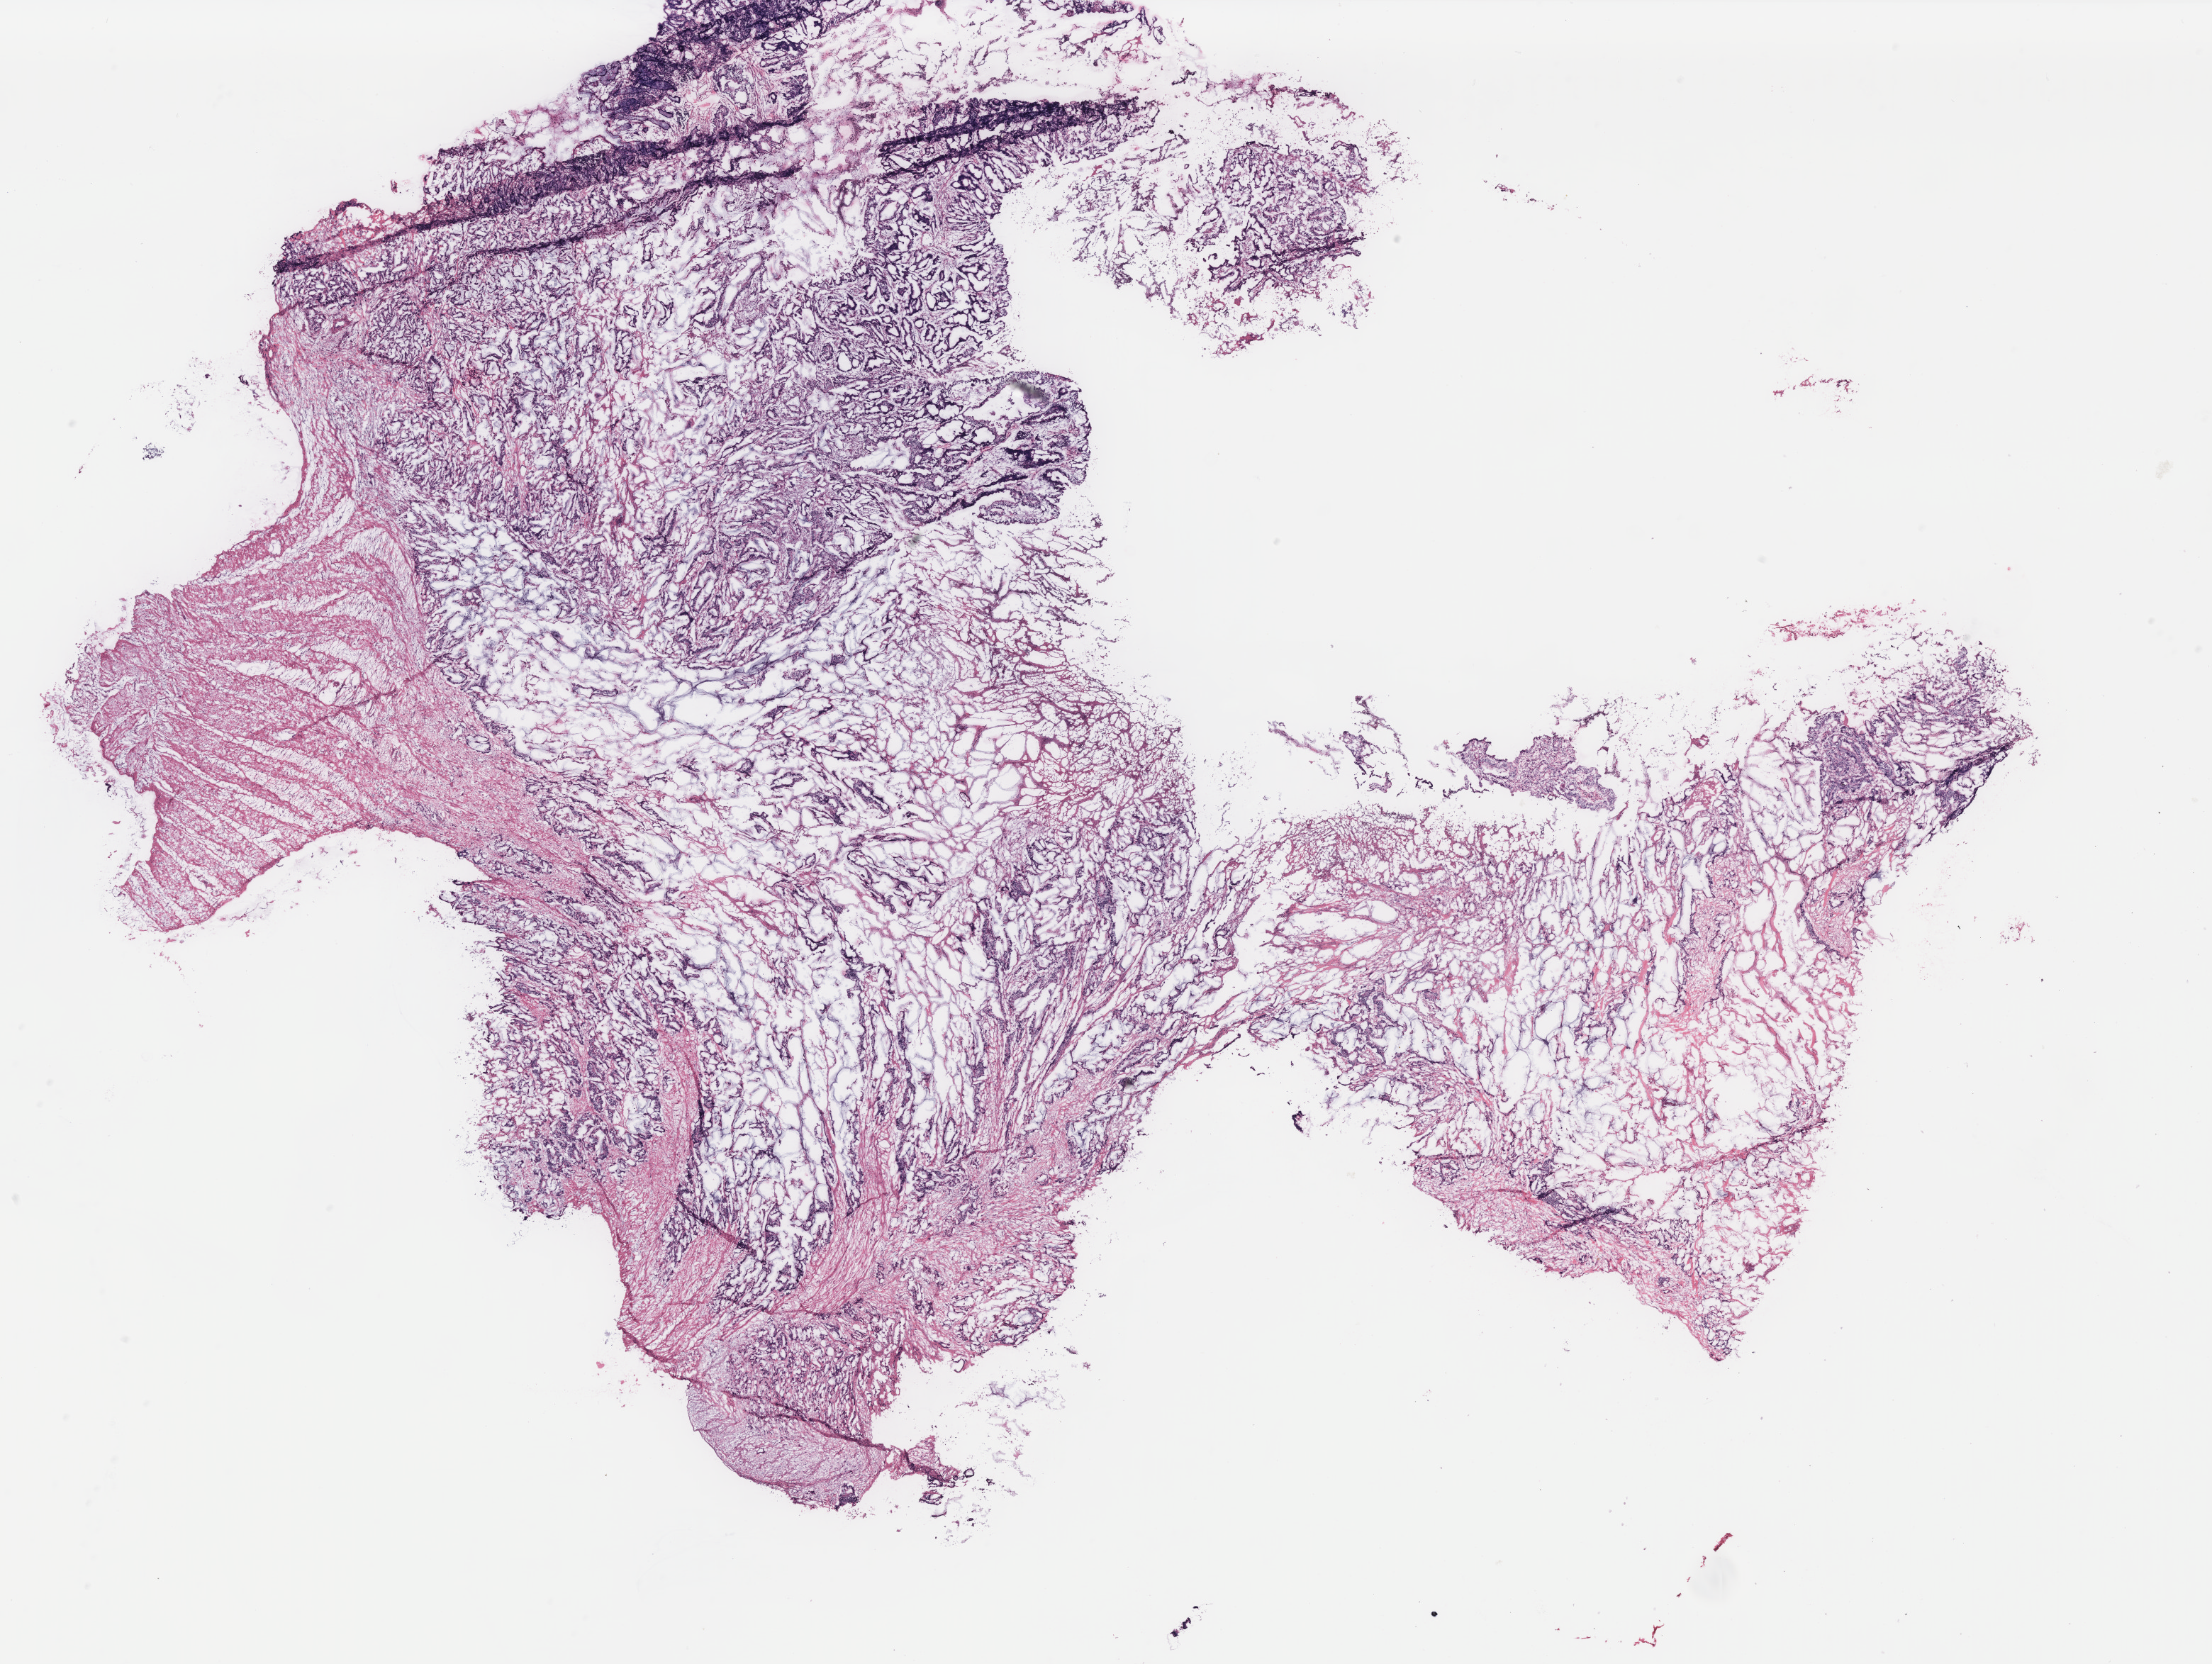
H&E whole-slide image, whole scanned area (about 25.0 x 18.8 mm, acquisition: 40x scan) shown as a low-resolution overview. Colon, tissue type not recorded.
Patient diagnosis (cohort enrolment): colon cancer (colon).